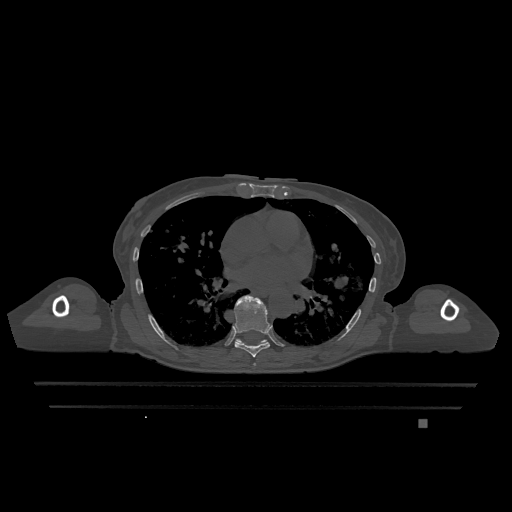
CT including the spine, one axial slice; position 729 of 1317 along the scan axis; bone window (W 1800 / L 400 HU); 0.5 mm slice thickness; 512 × 512 image matrix, field of view 500 × 500 mm. Patient: female, 74 years. Case-level facts recorded for this patient, not image findings: primary cancer: lung.
Structures marked on this image (semi-automatic segmentation, software-assisted and operator-edited):
- T6 vertebra: bounding box (x1, y1, x2, y2) in pixels: (254, 363, 256, 366)
- T7 vertebra: (234, 295, 270, 357)
- T9 vertebra: (236, 339, 267, 345)